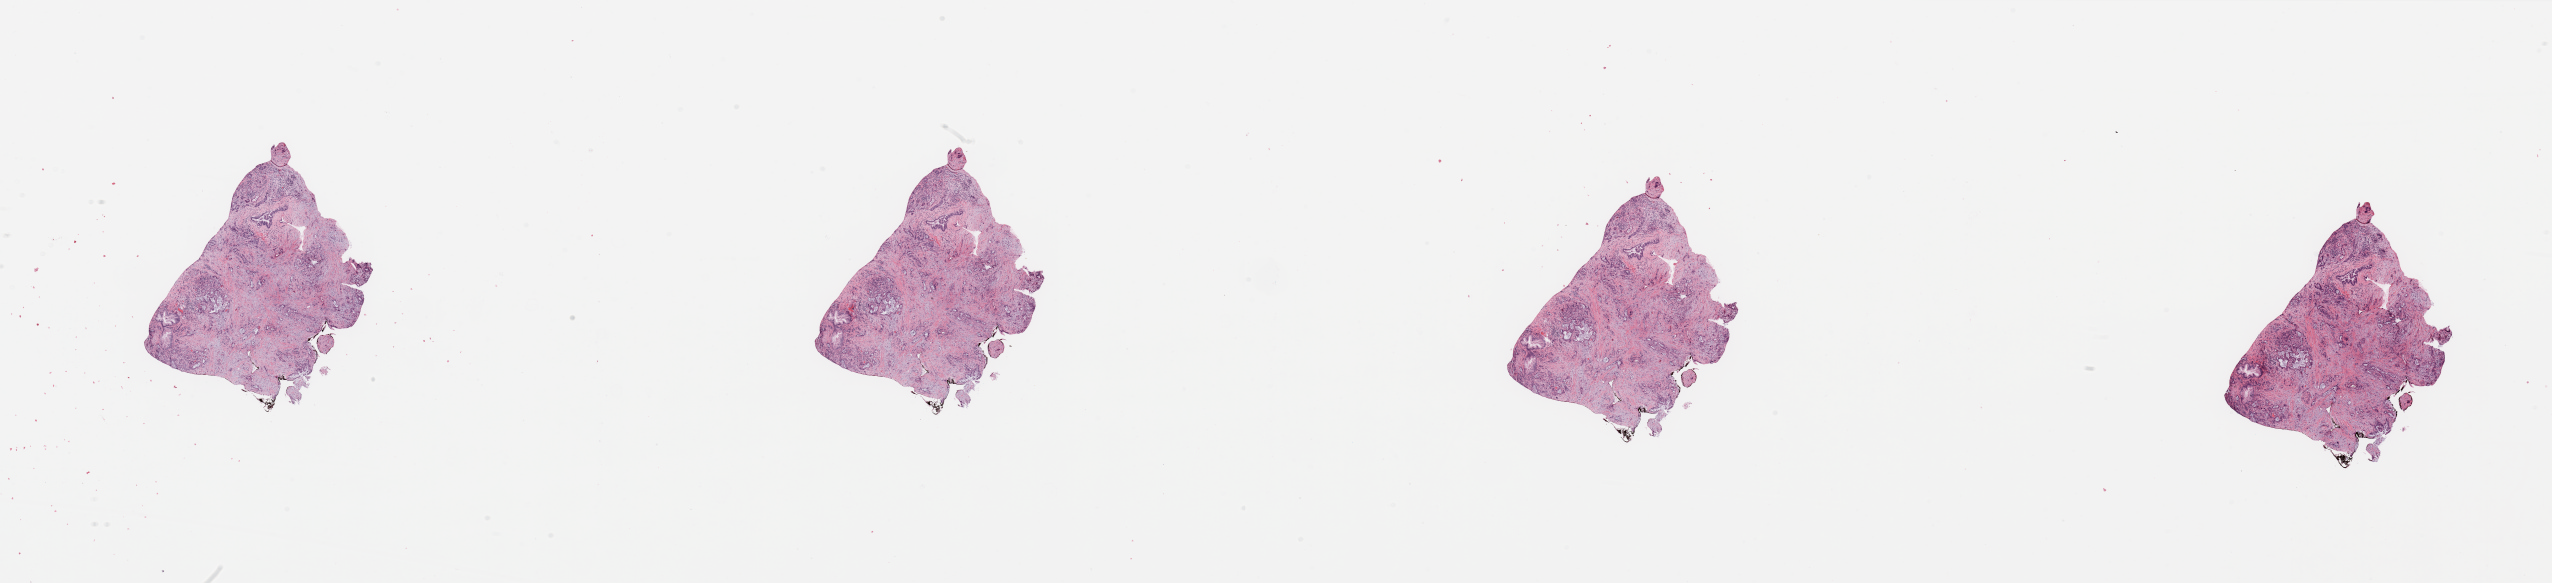
Whole-slide histology image, H&E, a low-resolution overview of the entire scanned area, about 40.4 x 9.2 mm (acquisition: 20x scan), tumour tissue sample, sampled site: pancreas. Patient: female, age 67 years. Histologic grade: G2 (moderately differentiated). Composition of this section per pathologist review: tumour nuclei 60%, necrosis 0%.
AJCC pathologic stage: IB. Primary tumour site (as recorded): head. Diagnosis: Infiltrating duct carcinoma, NOS.